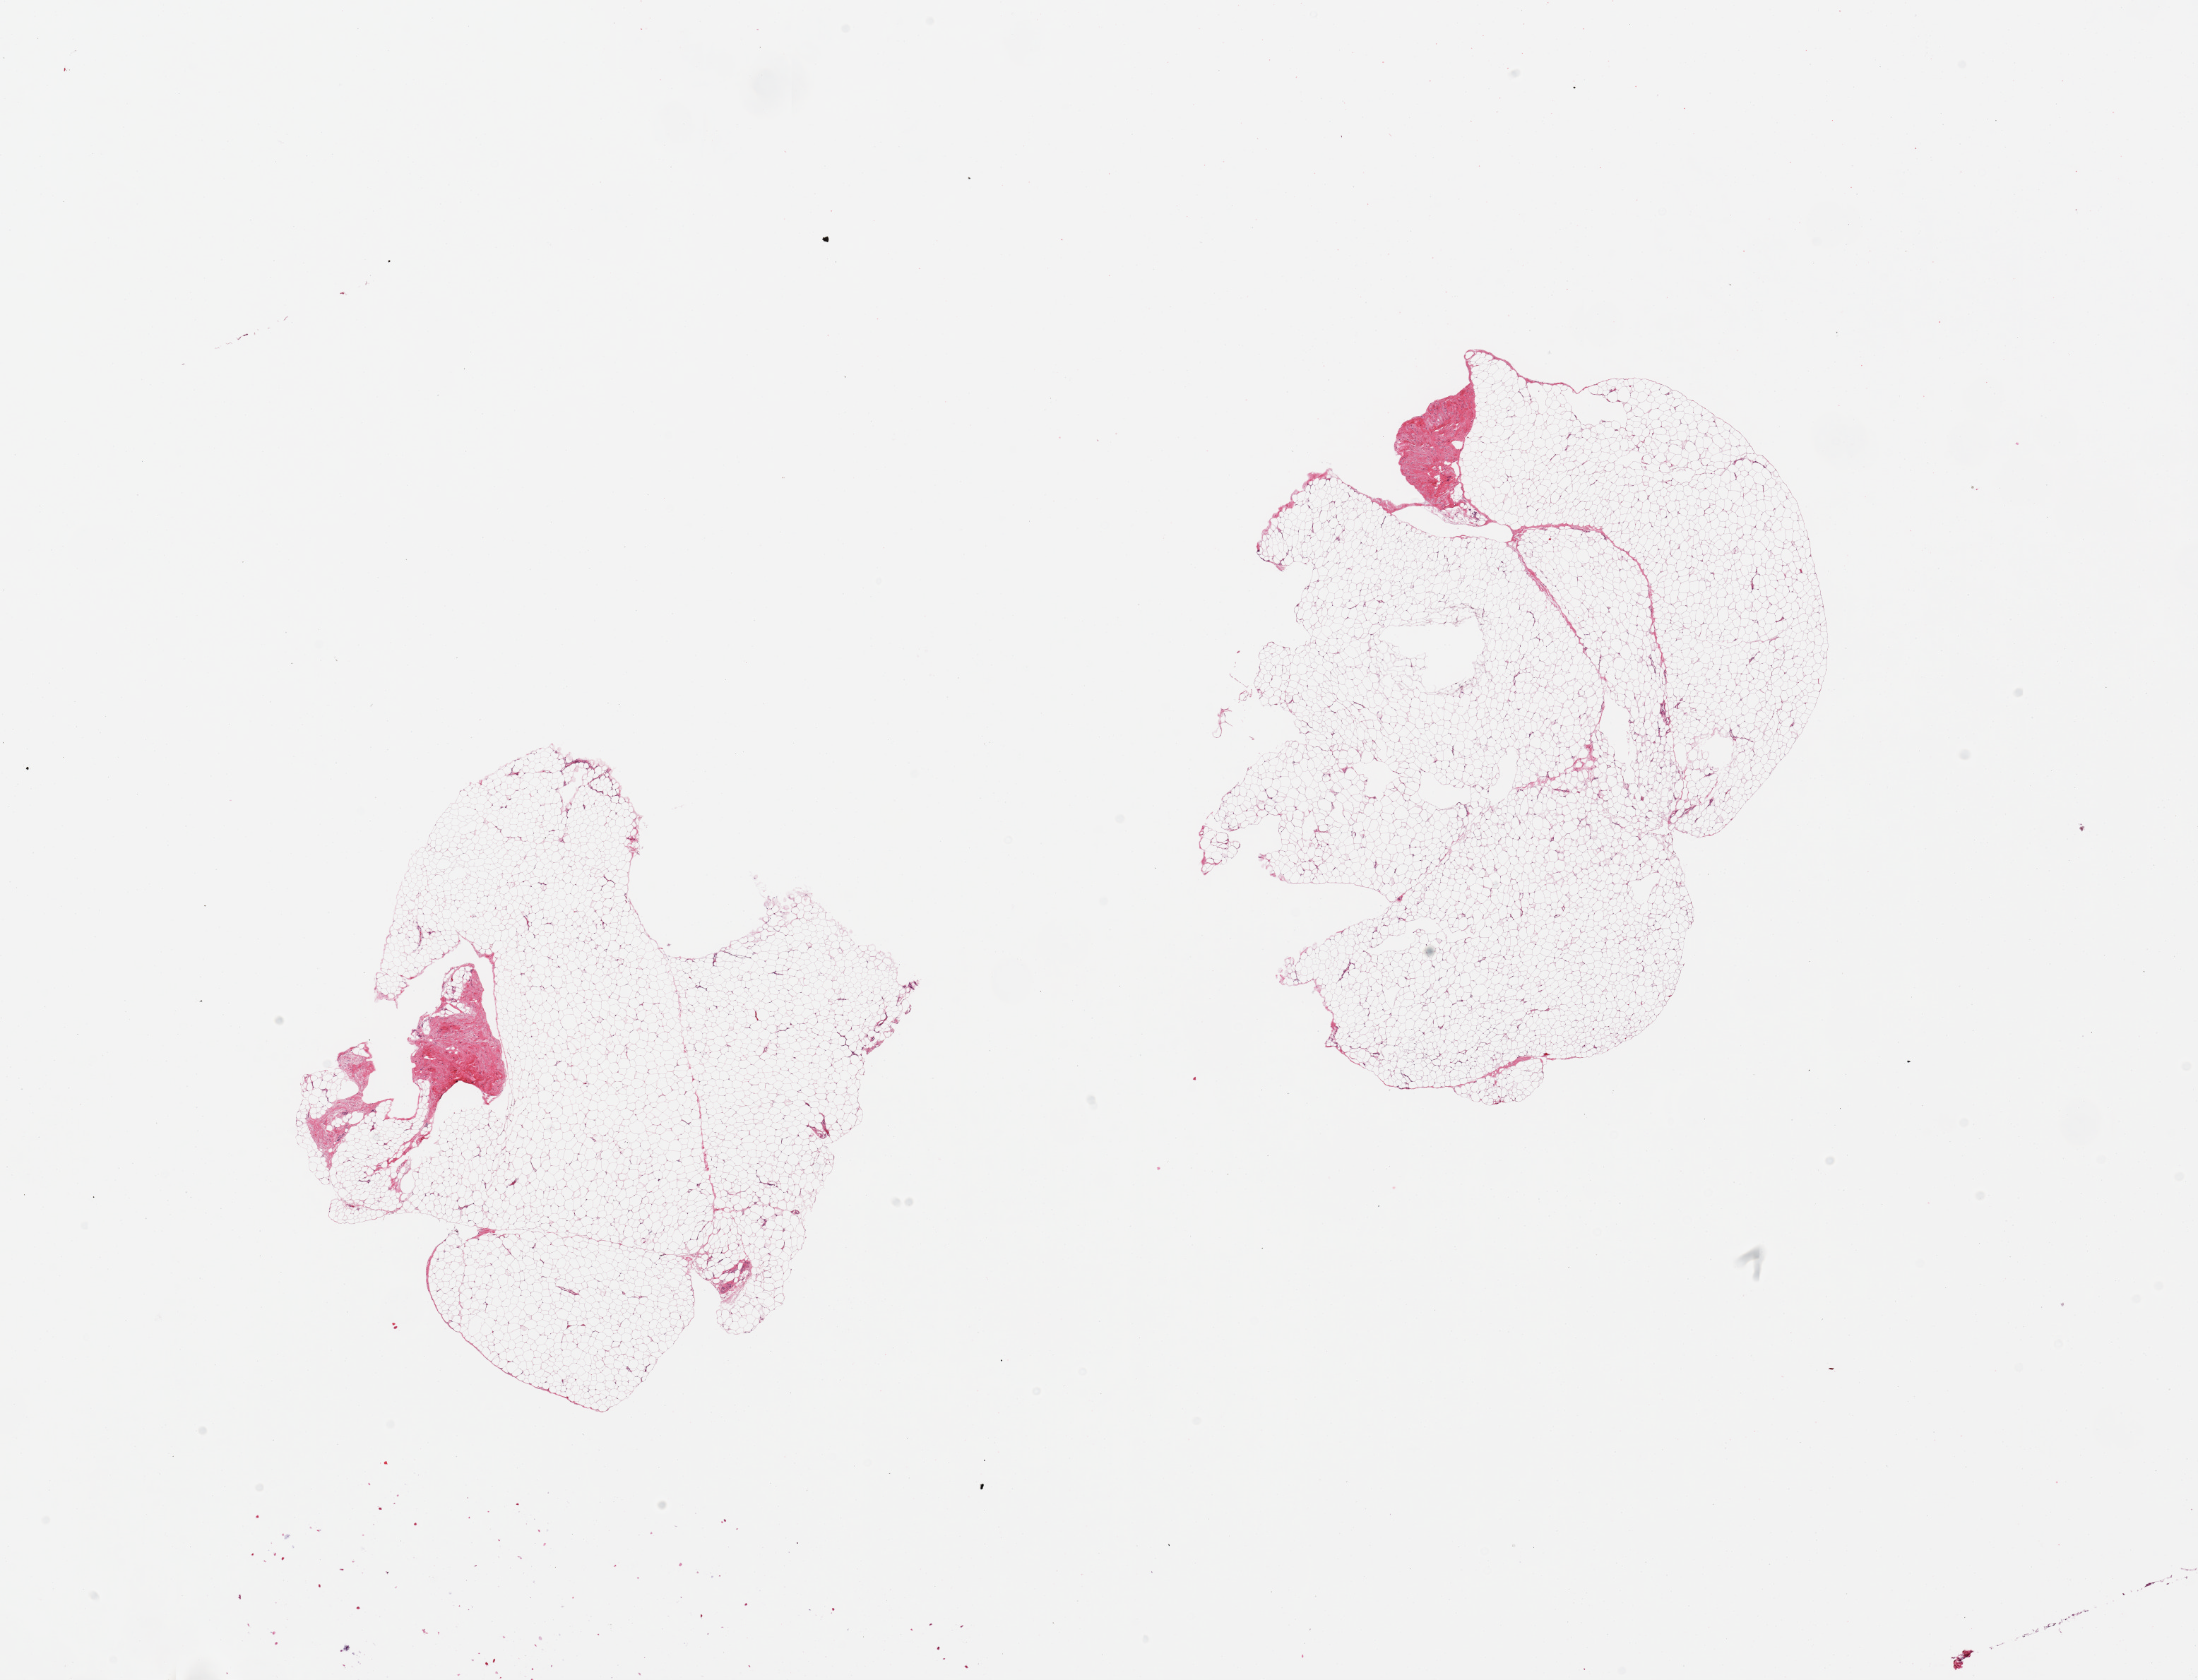
Haematoxylin and eosin whole-slide image, brightfield — low-resolution overview of the scanned area, about 24.6 x 18.8 mm (from a 20x scan), PAXgene-fixed, paraffin-embedded tissue, sampled site (target tissue): adipose tissue, donor tissue sample. Donor sex: male.
* pathologist's review note for this sample: 2 pieces; 5% fibrous content